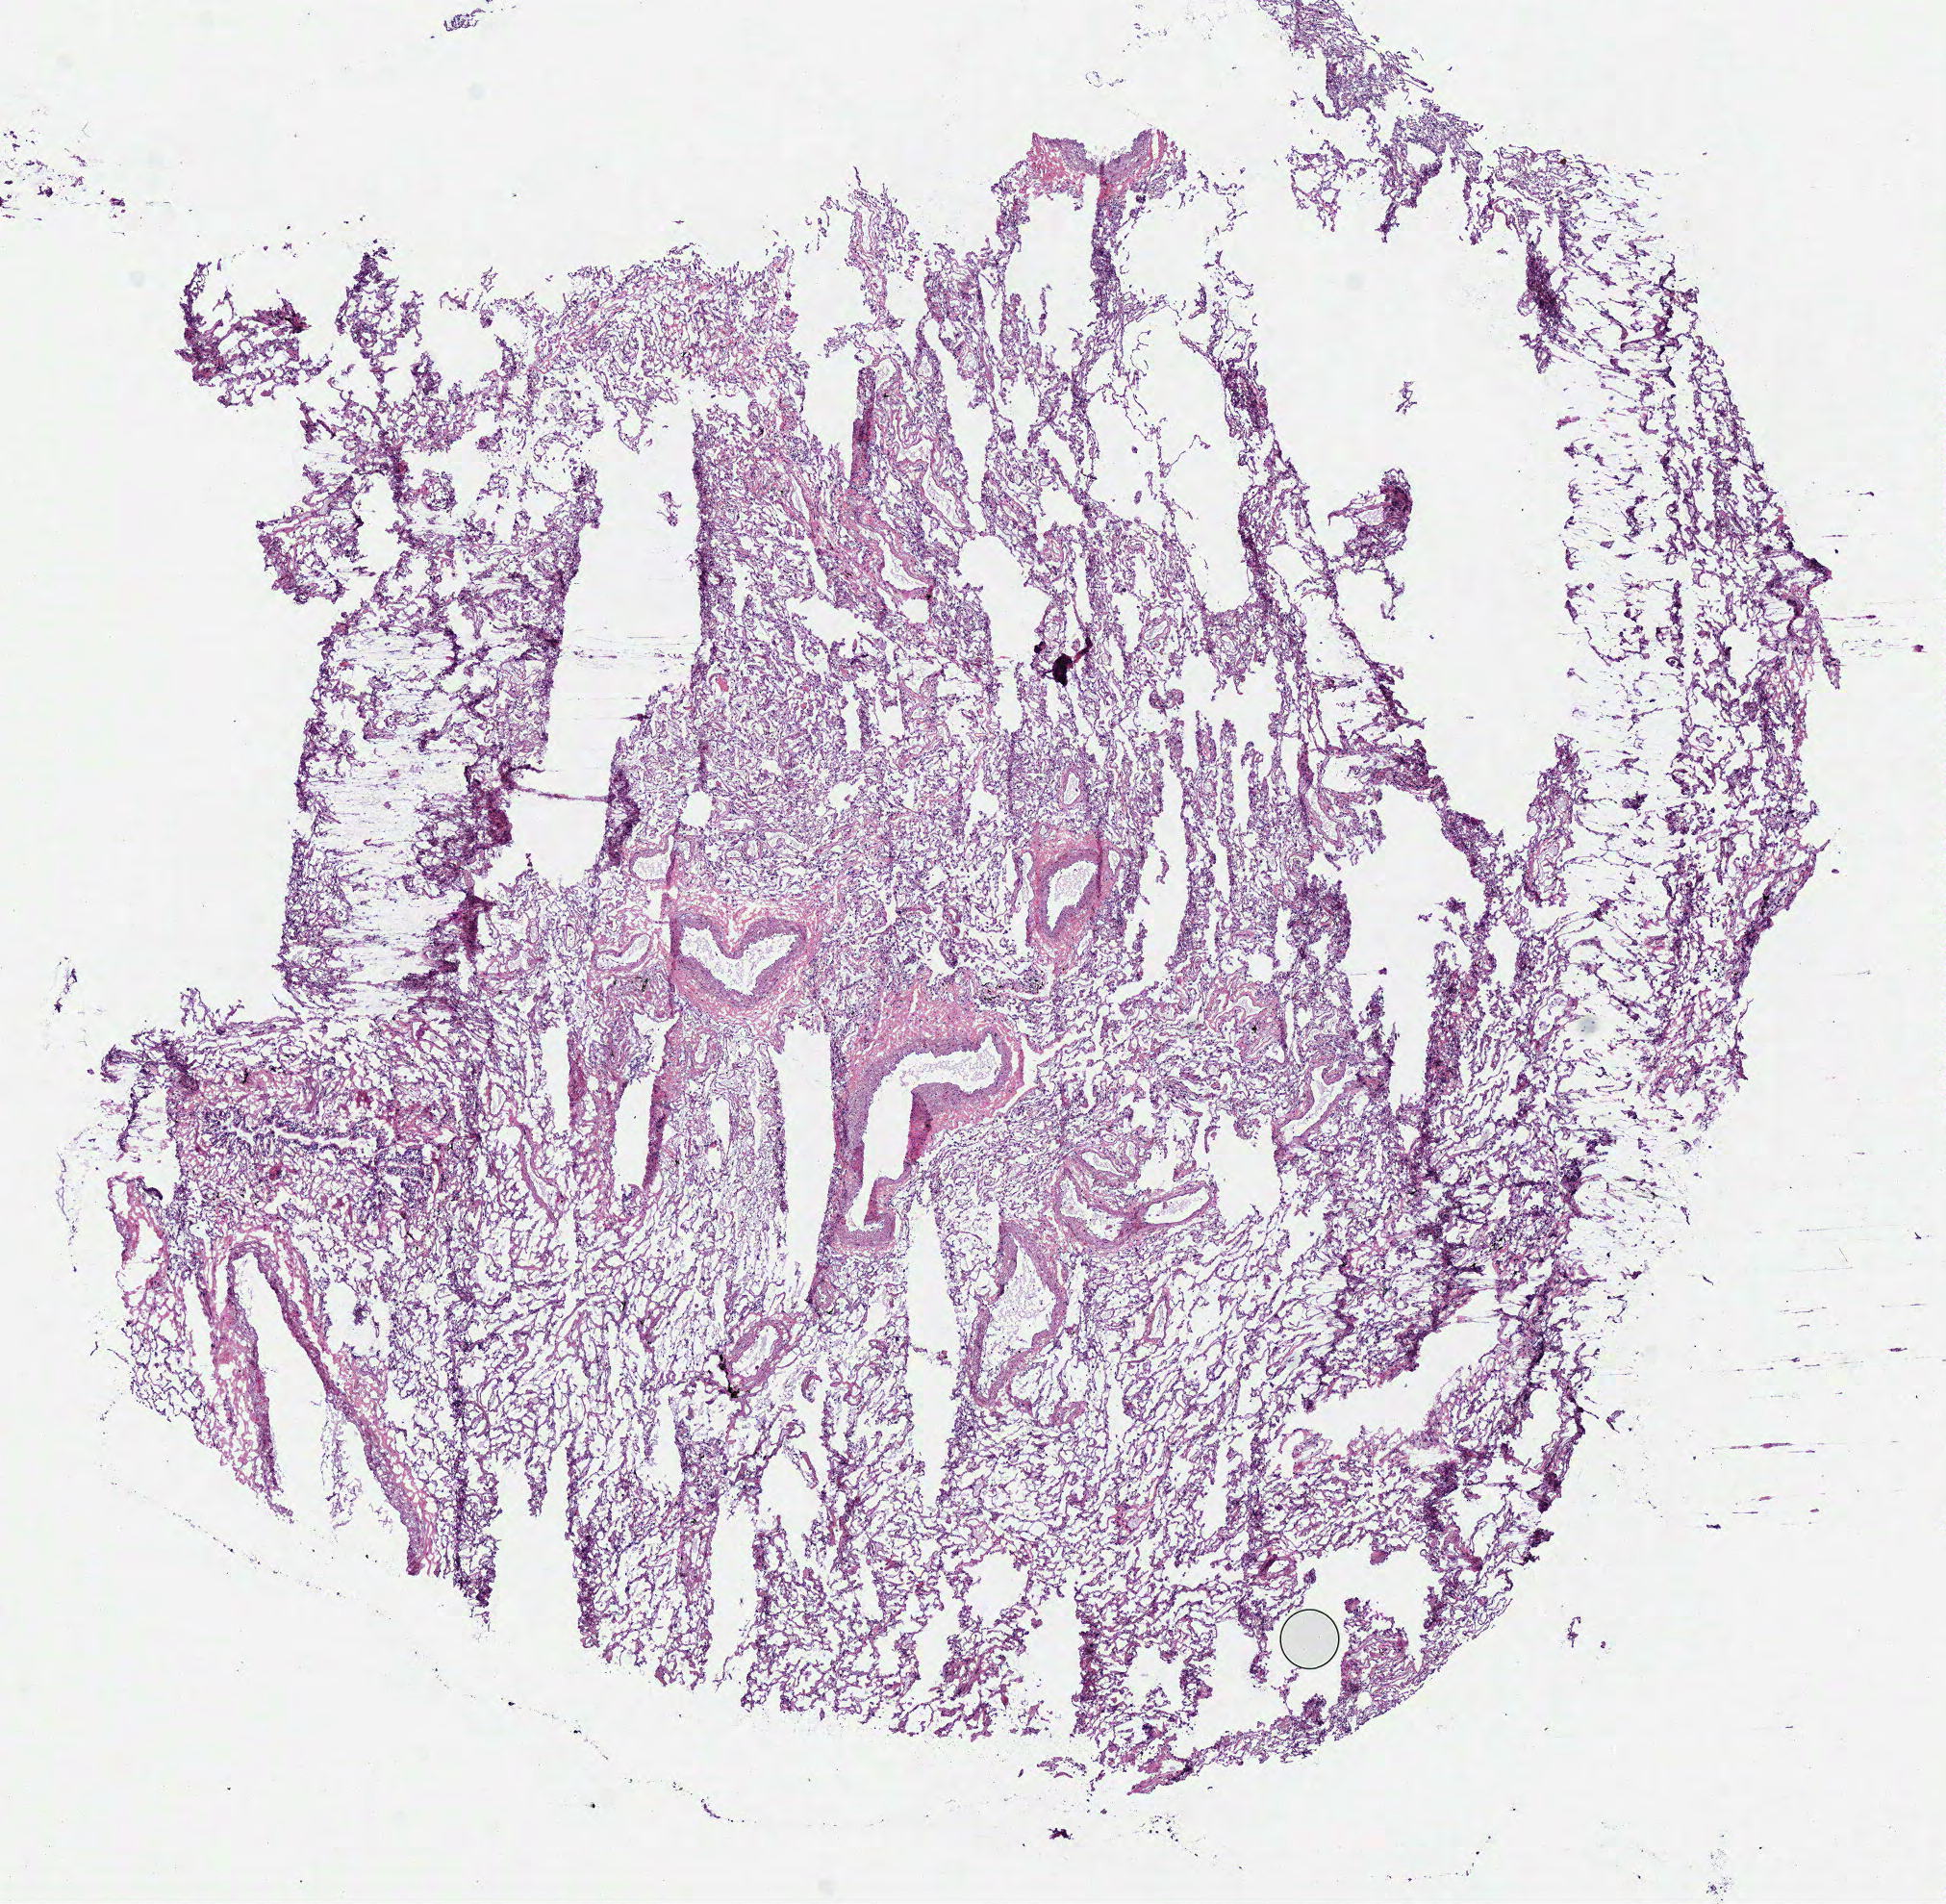
Digitized H&E-stained tissue section (whole slide), low-resolution overview of the scanned area, about 8.0 x 7.8 mm (from a 40x scan), frozen section from the top of the tissue portion, solid tissue normal (non-tumour tissue) sample from the lung. Patient: male, age at initial diagnosis 71 years.
• this section: solid tissue normal (non-tumour) sample from the same patient
• patient diagnosis: Squamous cell carcinoma, NOS (upper lobe, lung)